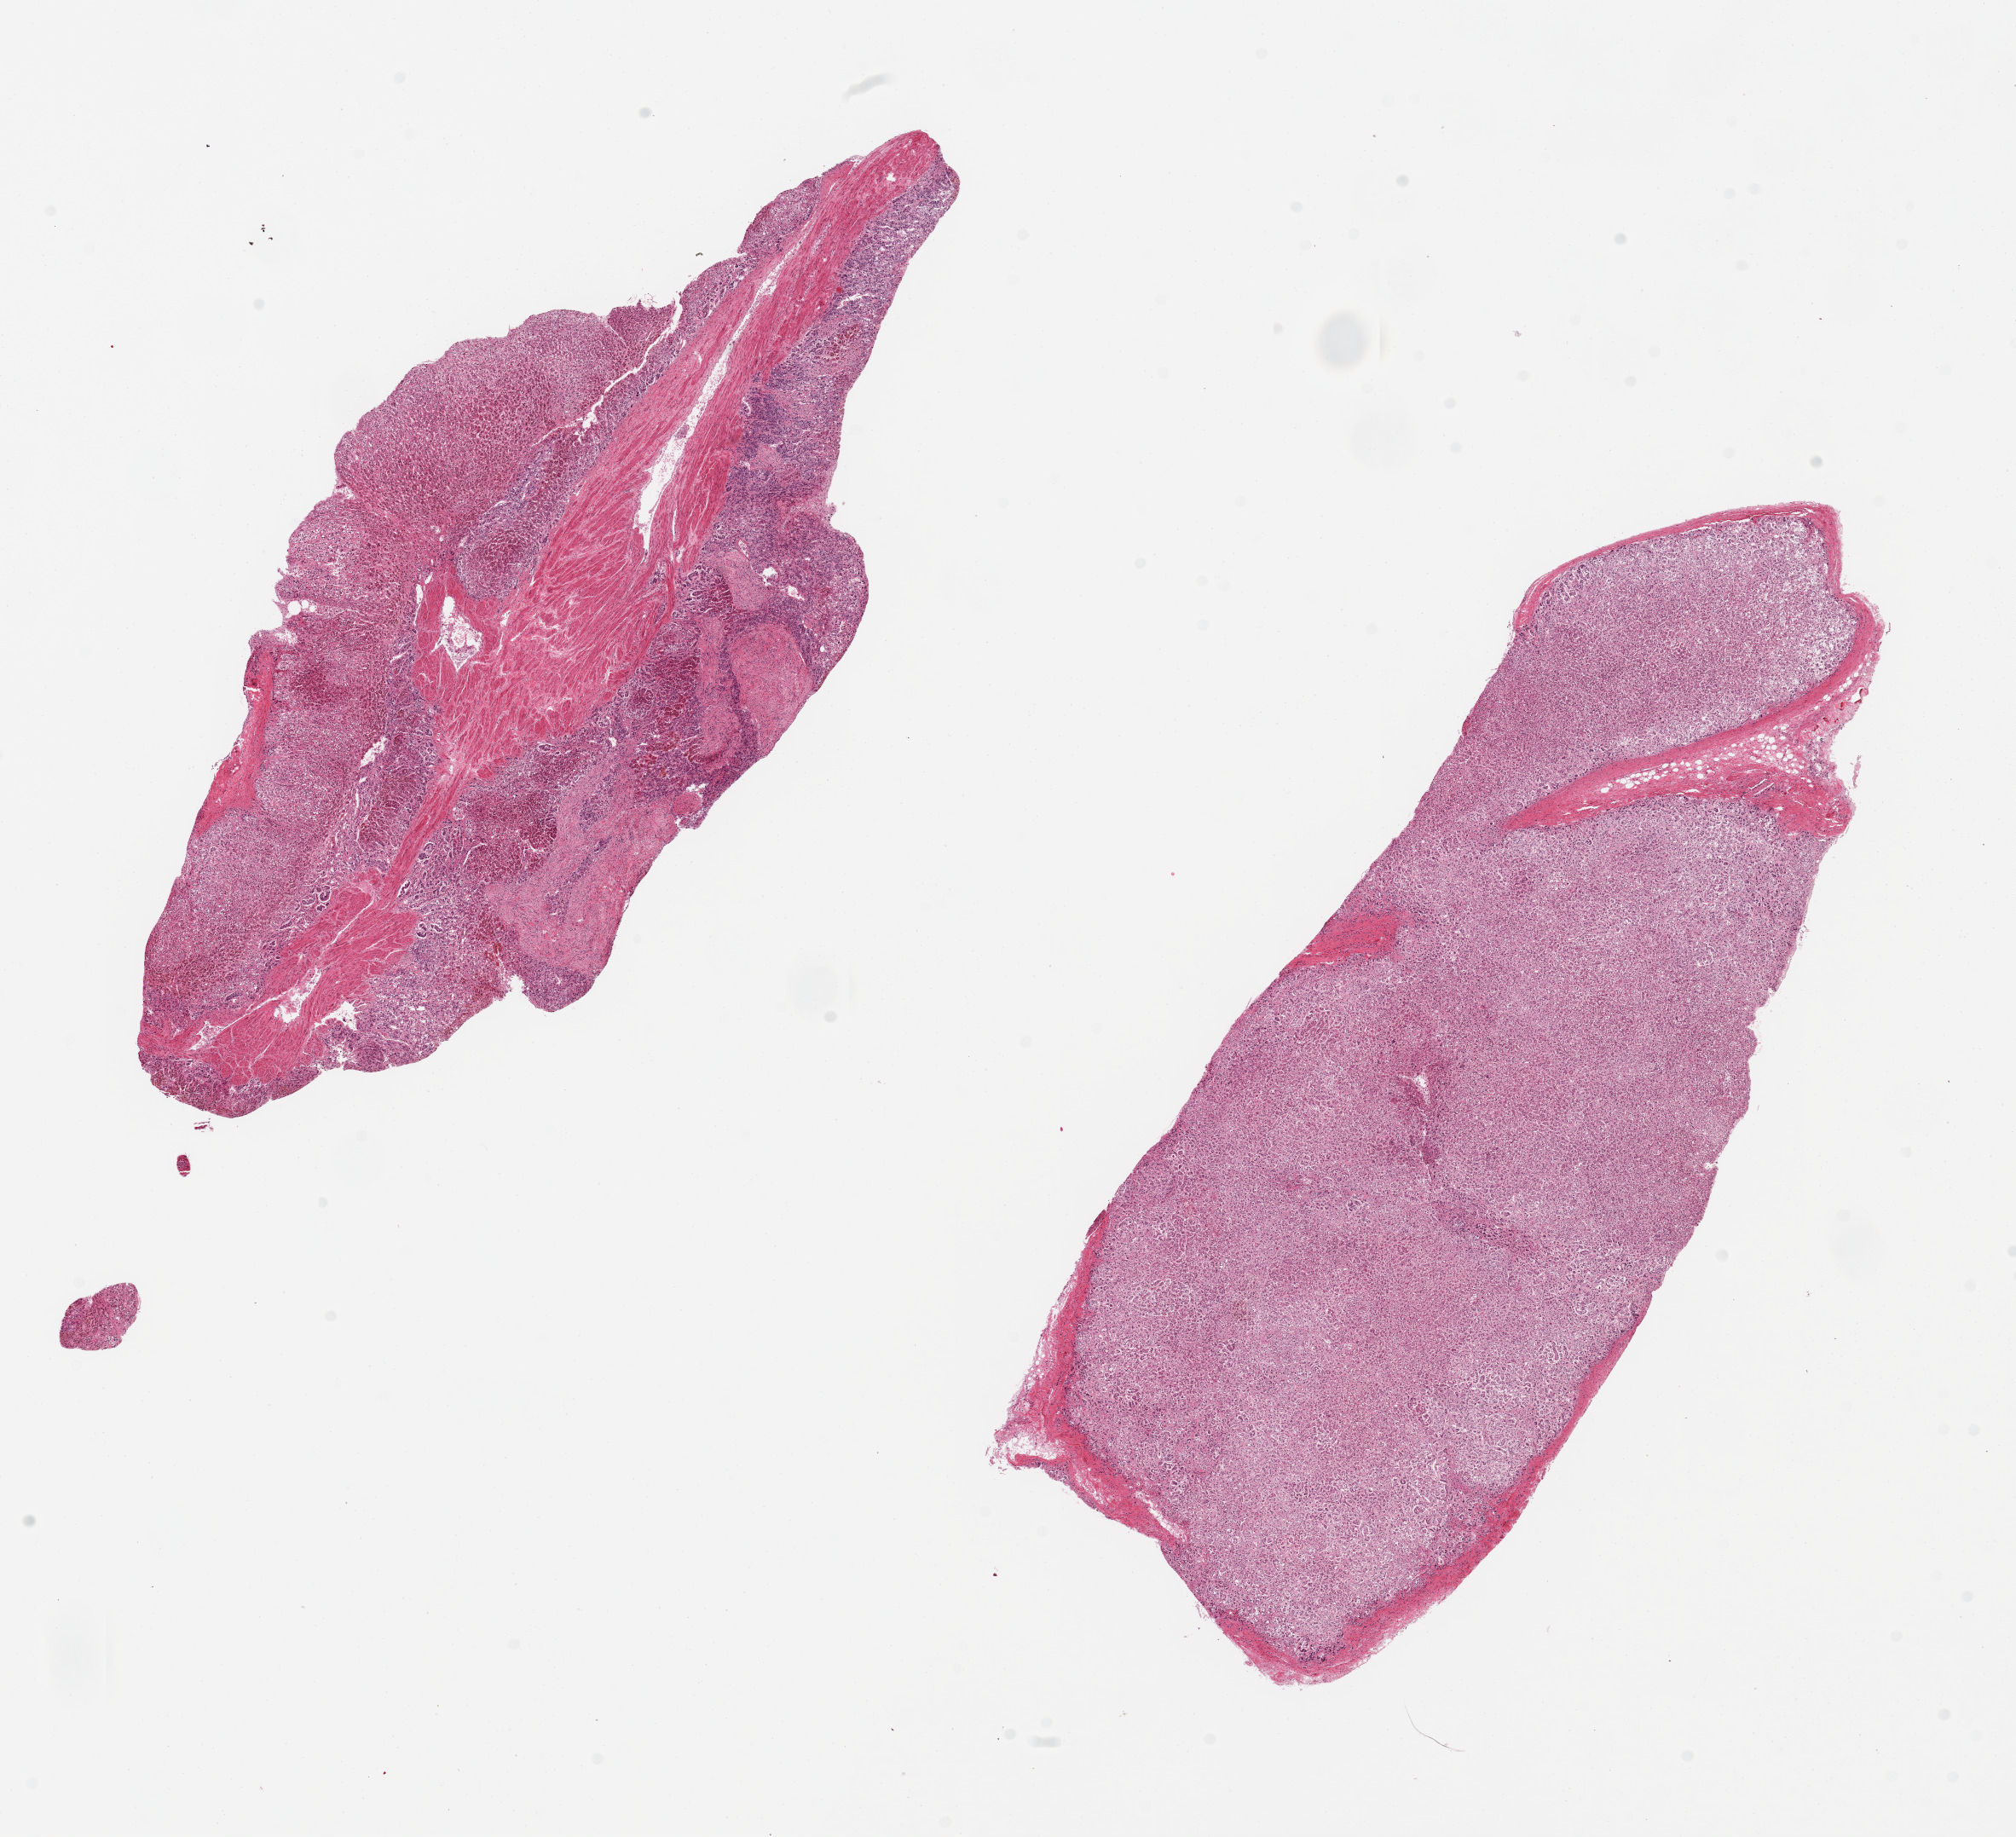
Digitized H&E-stained section, whole scanned area (about 18.7 x 17.0 mm, slide scanned at 20x) shown as a low-resolution overview. PAXgene-fixed paraffin-embedded (PFPE) section. Target tissue: adrenal gland. Donor tissue sample.
Pathologist's review note for this sample: 2 pieces; 1 almost pure cortex, other mixture of layers high (30%) vascular content.